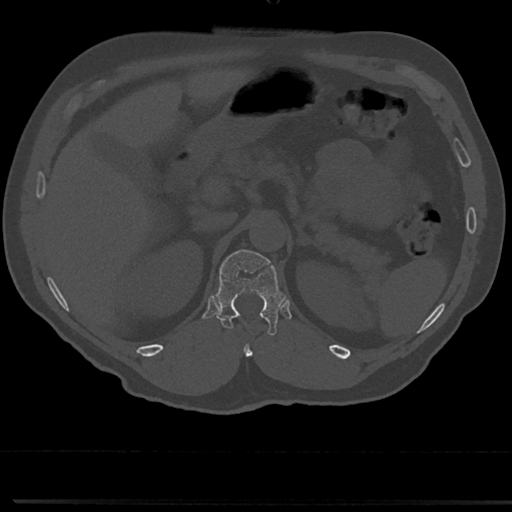
CT including the spine, one axial slice; slice 155 of 817 in the series (ordered by position); reconstruction kernel Br40s/3; 120 kVp; bone window (W 1800 / L 400 HU); 0.5 mm slice thickness; 512 × 512 image matrix, field of view 355 × 355 mm. Male patient, age 61 years. Case-level facts recorded for this patient, not image findings: primary cancer: prostate.
Outlined on this slice (semi-automatic segmentation, software-assisted and operator-edited):
- T12 vertebra: bounding box (x1, y1, x2, y2) in pixels: (215, 247, 281, 333)